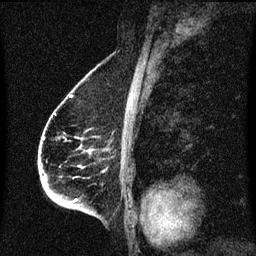
Breast MRI (dynamic contrast-enhanced), one sagittal slice; slice 42 of 60 in the series (ordered by position); dynamic contrast-enhanced series, image 2 of 3 at this slice position (ordered by acquisition); 1.5 T; TE 4.2 ms, TR 8.4 ms; 2 mm slice thickness; 256 × 256 image matrix, field of view 200 × 200 mm. Female patient, age 68 years. From the clinical record (not read from this slice): setting: breast cancer imaged before/during neoadjuvant chemotherapy; receptor status: triple-negative.
Annotated regions visible in this slice (semi-automatic segmentation, software-assisted and operator-edited):
- analysis volume of interest (the breast-tissue region the enhancement analysis was run in; not a lesion): bounding box [x1, y1, x2, y2] px = [40, 96, 110, 213]
- tumour enhancement mask (voxels above the 70 % enhancement threshold inside the analysis volume of interest): [76, 166, 81, 201]